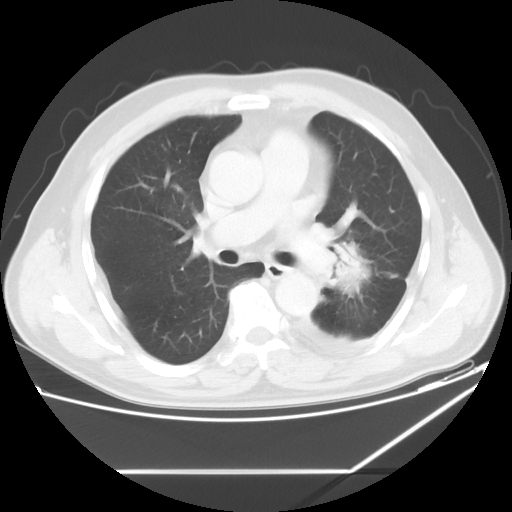
Chest CT, one axial slice; position 34 of 60 along the scan axis; lung window (W 1500 / L -600 HU); 5 mm slice thickness; 512 × 512 image matrix, field of view 395 × 395 mm. Male patient, age 62 years. From the clinical record (not read from this slice): clinical TNM (as recorded): T3 N0 M1.
Outlined on this slice (rectangle marked by the reading radiologist):
- lung tumour (recorded histology: adenocarcinoma): bounding box [x1, y1, x2, y2] px = [333, 234, 369, 291]
- lung tumour (recorded histology: adenocarcinoma): [333, 237, 373, 289]